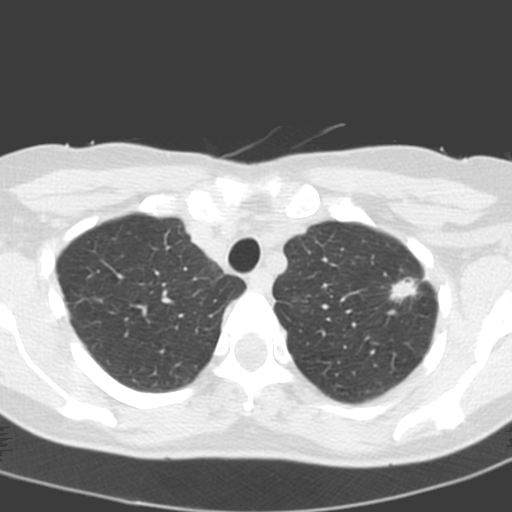
Low-dose screening chest CT, one axial slice; slice 159 of 193 in the series (ordered by position); 120 kVp; lung window (W 1500 / L -600 HU); 3.2 mm slice thickness; 512 × 512 image matrix, field of view 272 × 272 mm.
Outlined on this slice (outlined manually by an expert reader):
- lesion 1 (tumor, upper lobe of left lung): bounding box <390,277,418,302> (left, top, right, bottom; pixels)